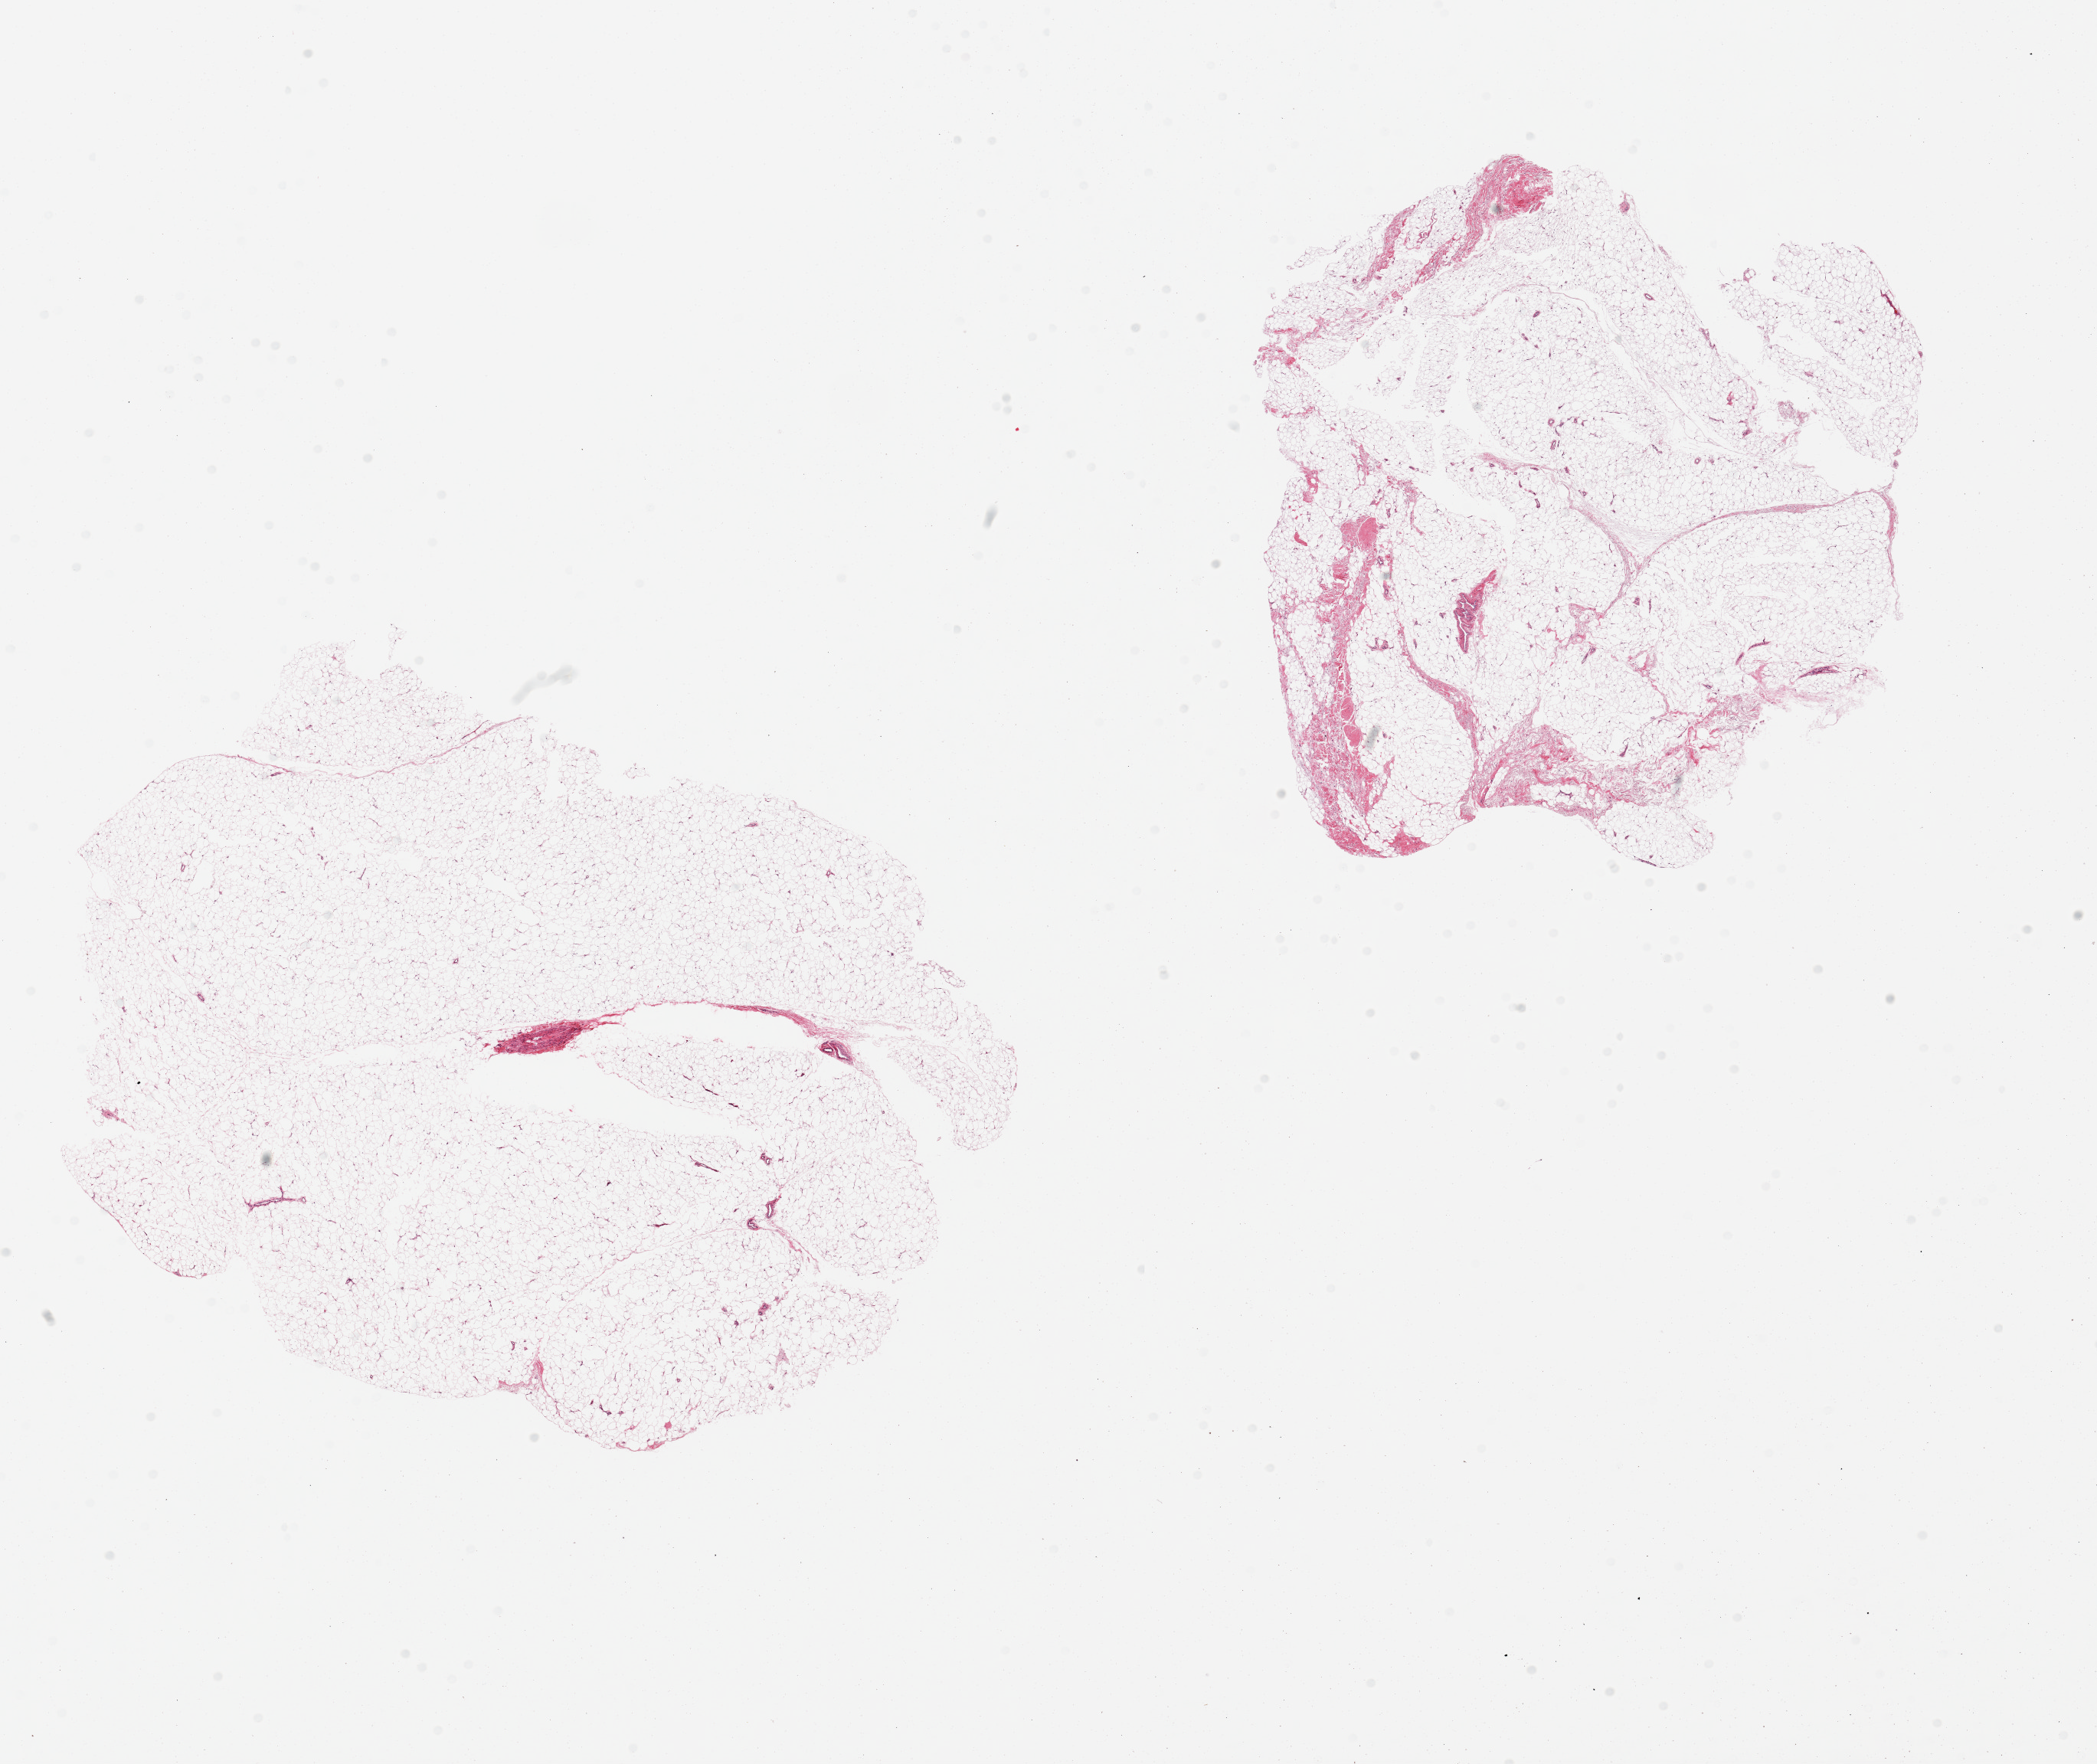
H&E whole-slide image, low-resolution overview of the scanned area, about 21.7 x 18.2 mm (from a 20x scan). PAXgene-fixed paraffin-embedded (PFPE) section. Sampled site (target tissue): adipose tissue. Donor tissue sample. Male donor.
• review note (as recorded): 2 pieces, ~5-10% fascia/vascular tissue